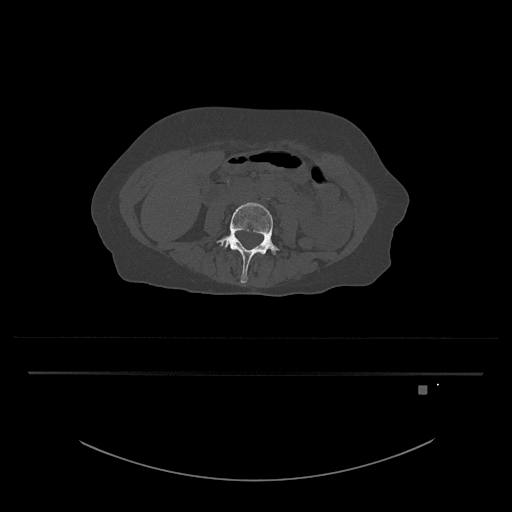
CT including the spine, one axial slice; slice 364 of 797 in the series (ordered by position); bone window (W 1800 / L 400 HU); 0.5 mm slice thickness; 512 × 512 image matrix, field of view 500 × 500 mm. Patient: female, 57 years. From the clinical record (not read from this slice): primary cancer: cervical.
Outlined on this slice (semi-automatically segmented with operator editing):
- L4 vertebra: box from (x=216, y=202) to (x=280, y=283) px